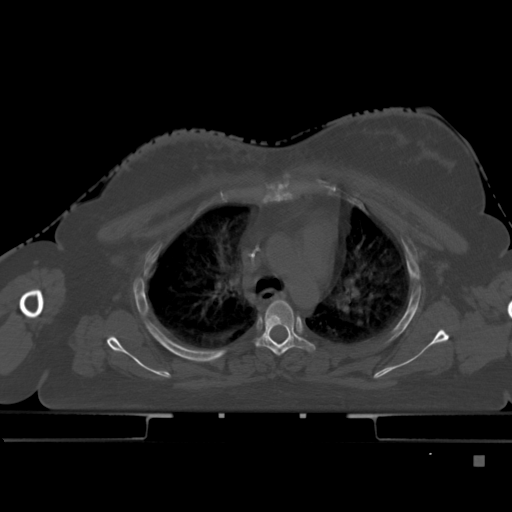
CT including the spine, one axial slice; position 334 of 495 along the scan axis; bone window (W 1800 / L 400 HU); 1.5 mm slice thickness; 512 × 512 image matrix. Patient: female, 33 years. From the clinical record (not read from this slice): primary cancer: breast; vertebrae with lytic lesions (as recorded): T1.
Outlined on this slice (semi-automatically segmented with operator editing):
- T4 vertebra: bounding box <256,299,315,356> (left, top, right, bottom; pixels)